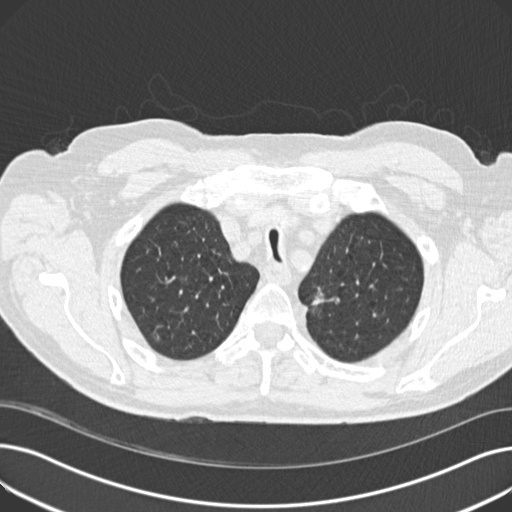
Chest CT (low-dose screening protocol), one axial image; third annual screen; lung window (W 1500 / L -600 HU); 2 mm slice thickness; standard (soft-tissue) reconstruction kernel (B30f); slice 41 of 191 in the series; 512 × 512 image matrix, field of view 370 × 370 mm. Male participant, aged 70 years at enrolment. Current smoker at enrolment.
Expert-annotated lung lesion, bounding box (x1, y1, x2, y2) in pixels: (291, 277, 338, 318). The screening reader recorded 2 non-calcified nodules or masses ≥4 mm on this exam (left upper lobe, left lower lobe); which of them this box marks is not recorded. Lung cancer was diagnosed 175 days after this screen: mixed cell adenocarcinoma, left upper lobe, poorly differentiated (G3), stage IIB (AJCC 6th edition), 17 mm at pathology.